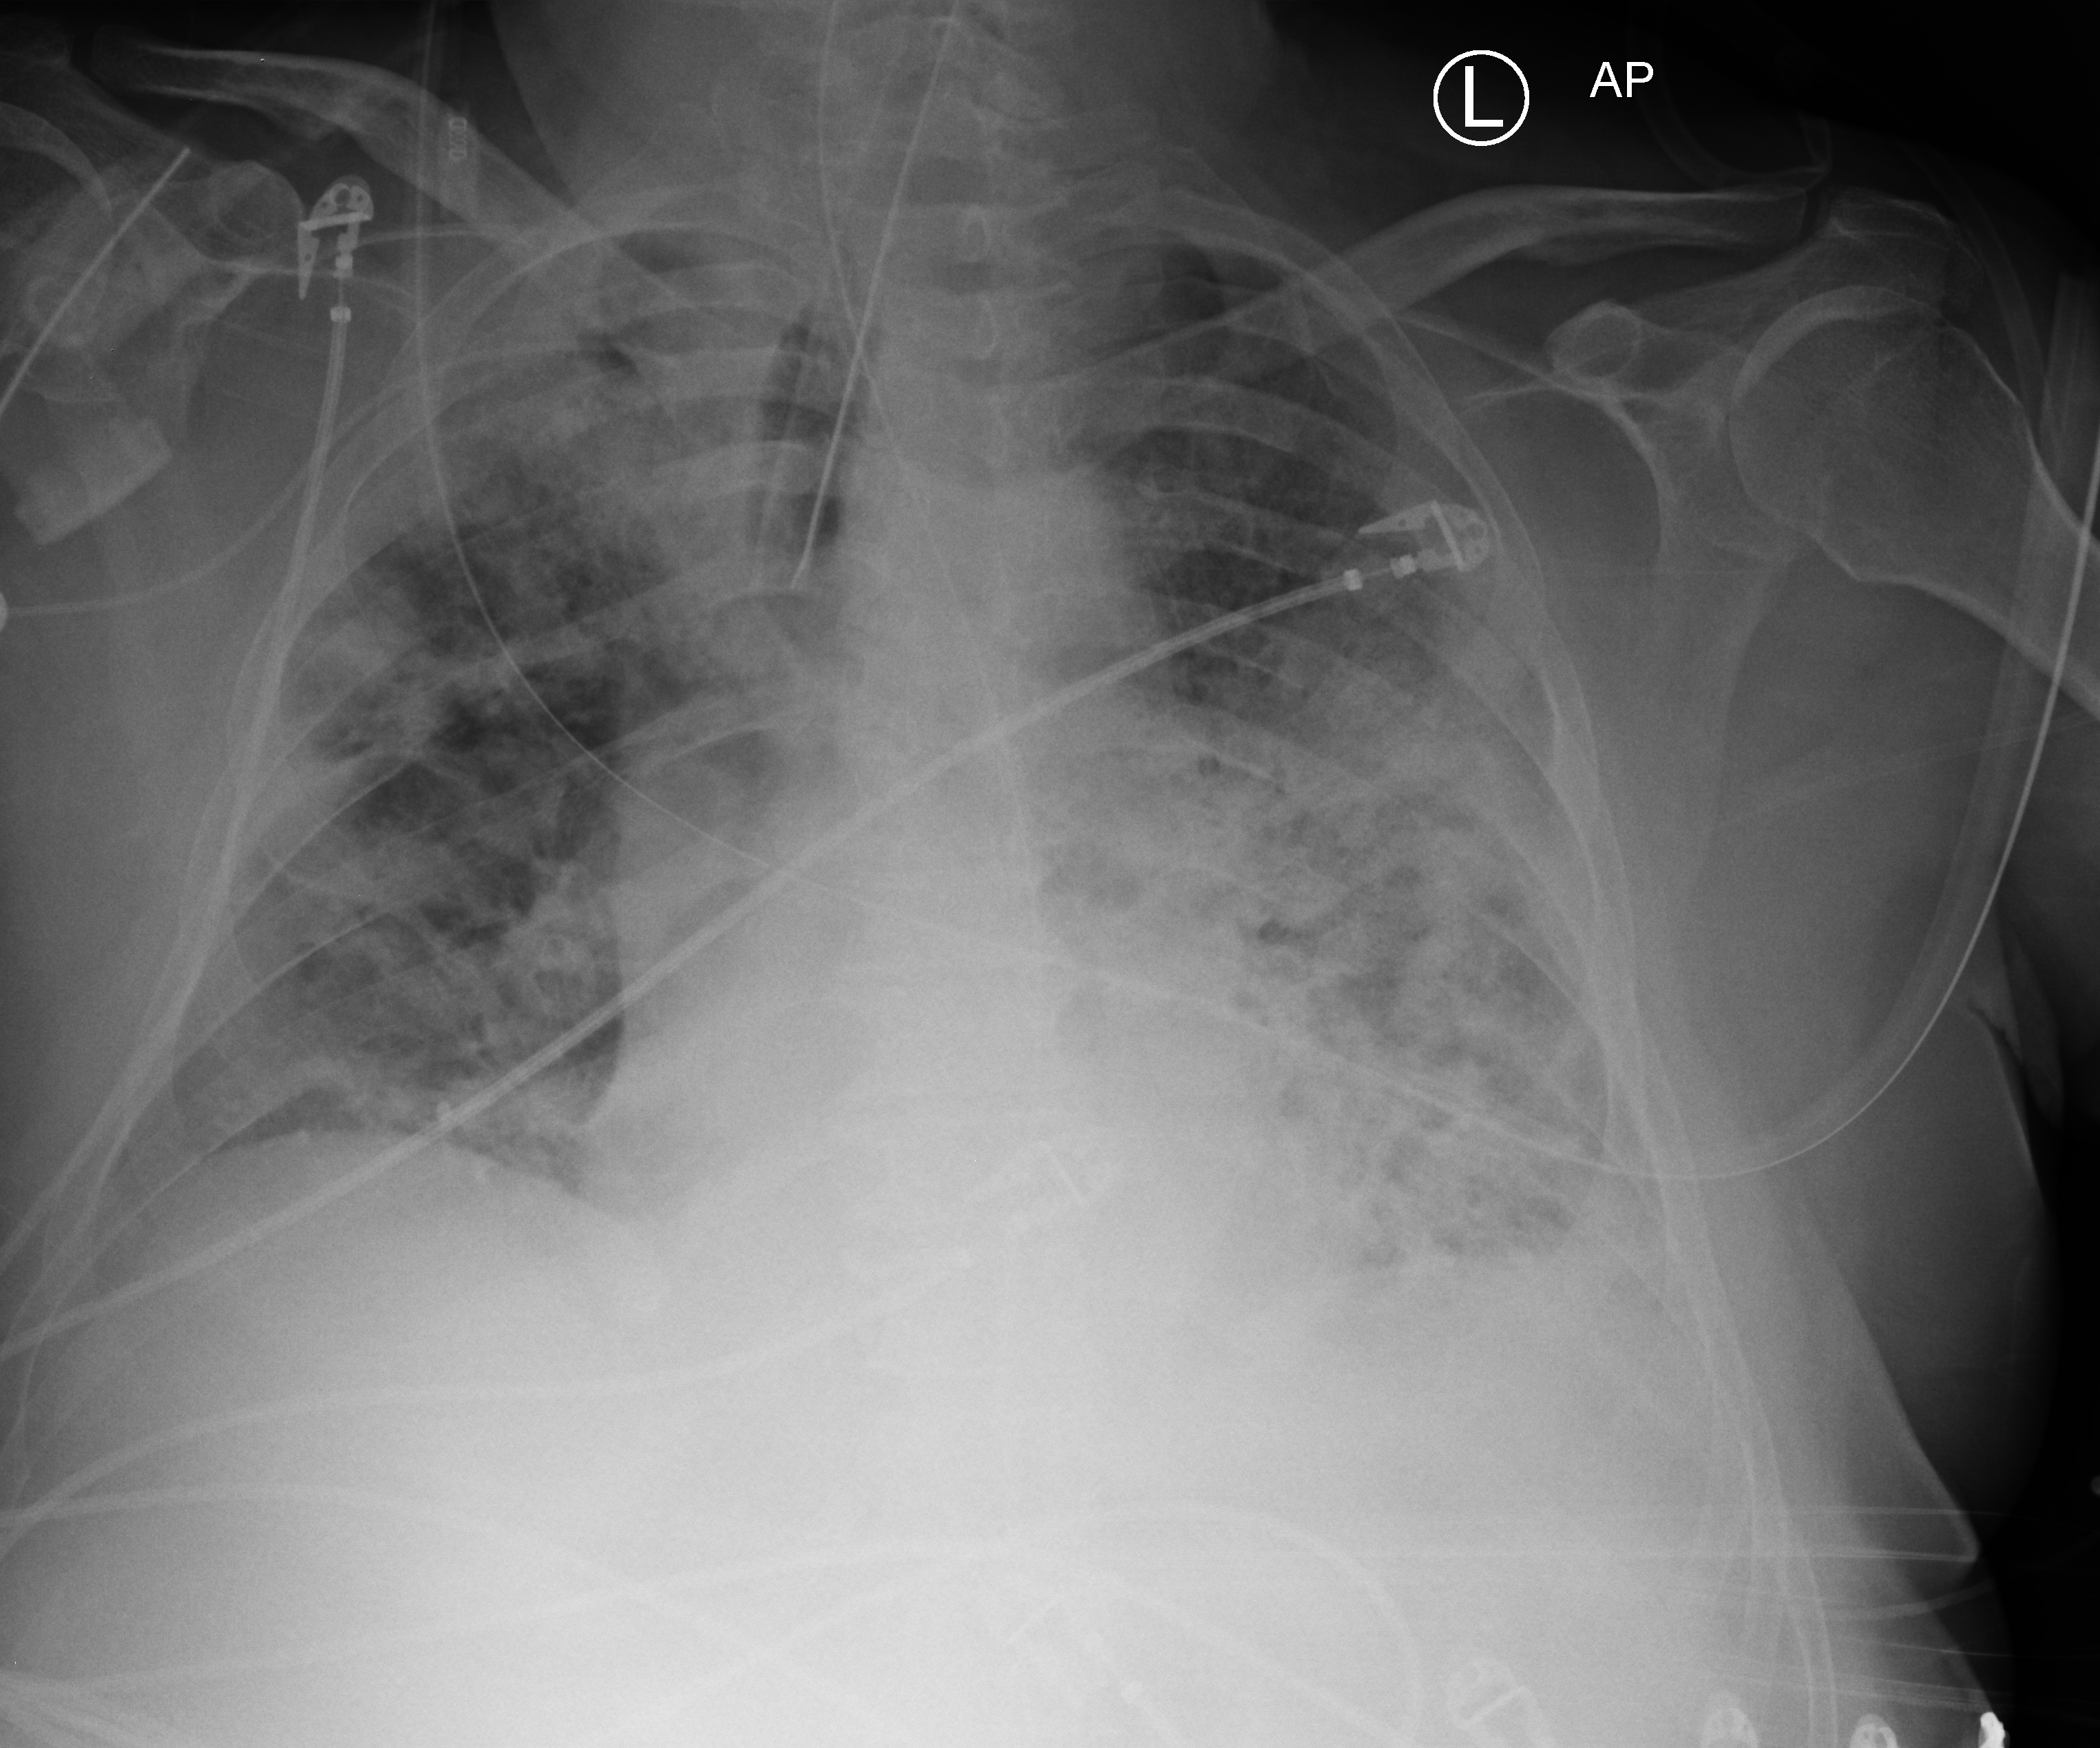
Bedside chest radiograph (computed radiography), anteroposterior (AP) projection. Patient hospitalised with COVID-19; male, aged 60–74 years.
From the hospital-stay record, not from the radiograph (when in the stay this image was taken is not recorded):
- hypertension (admission record): no